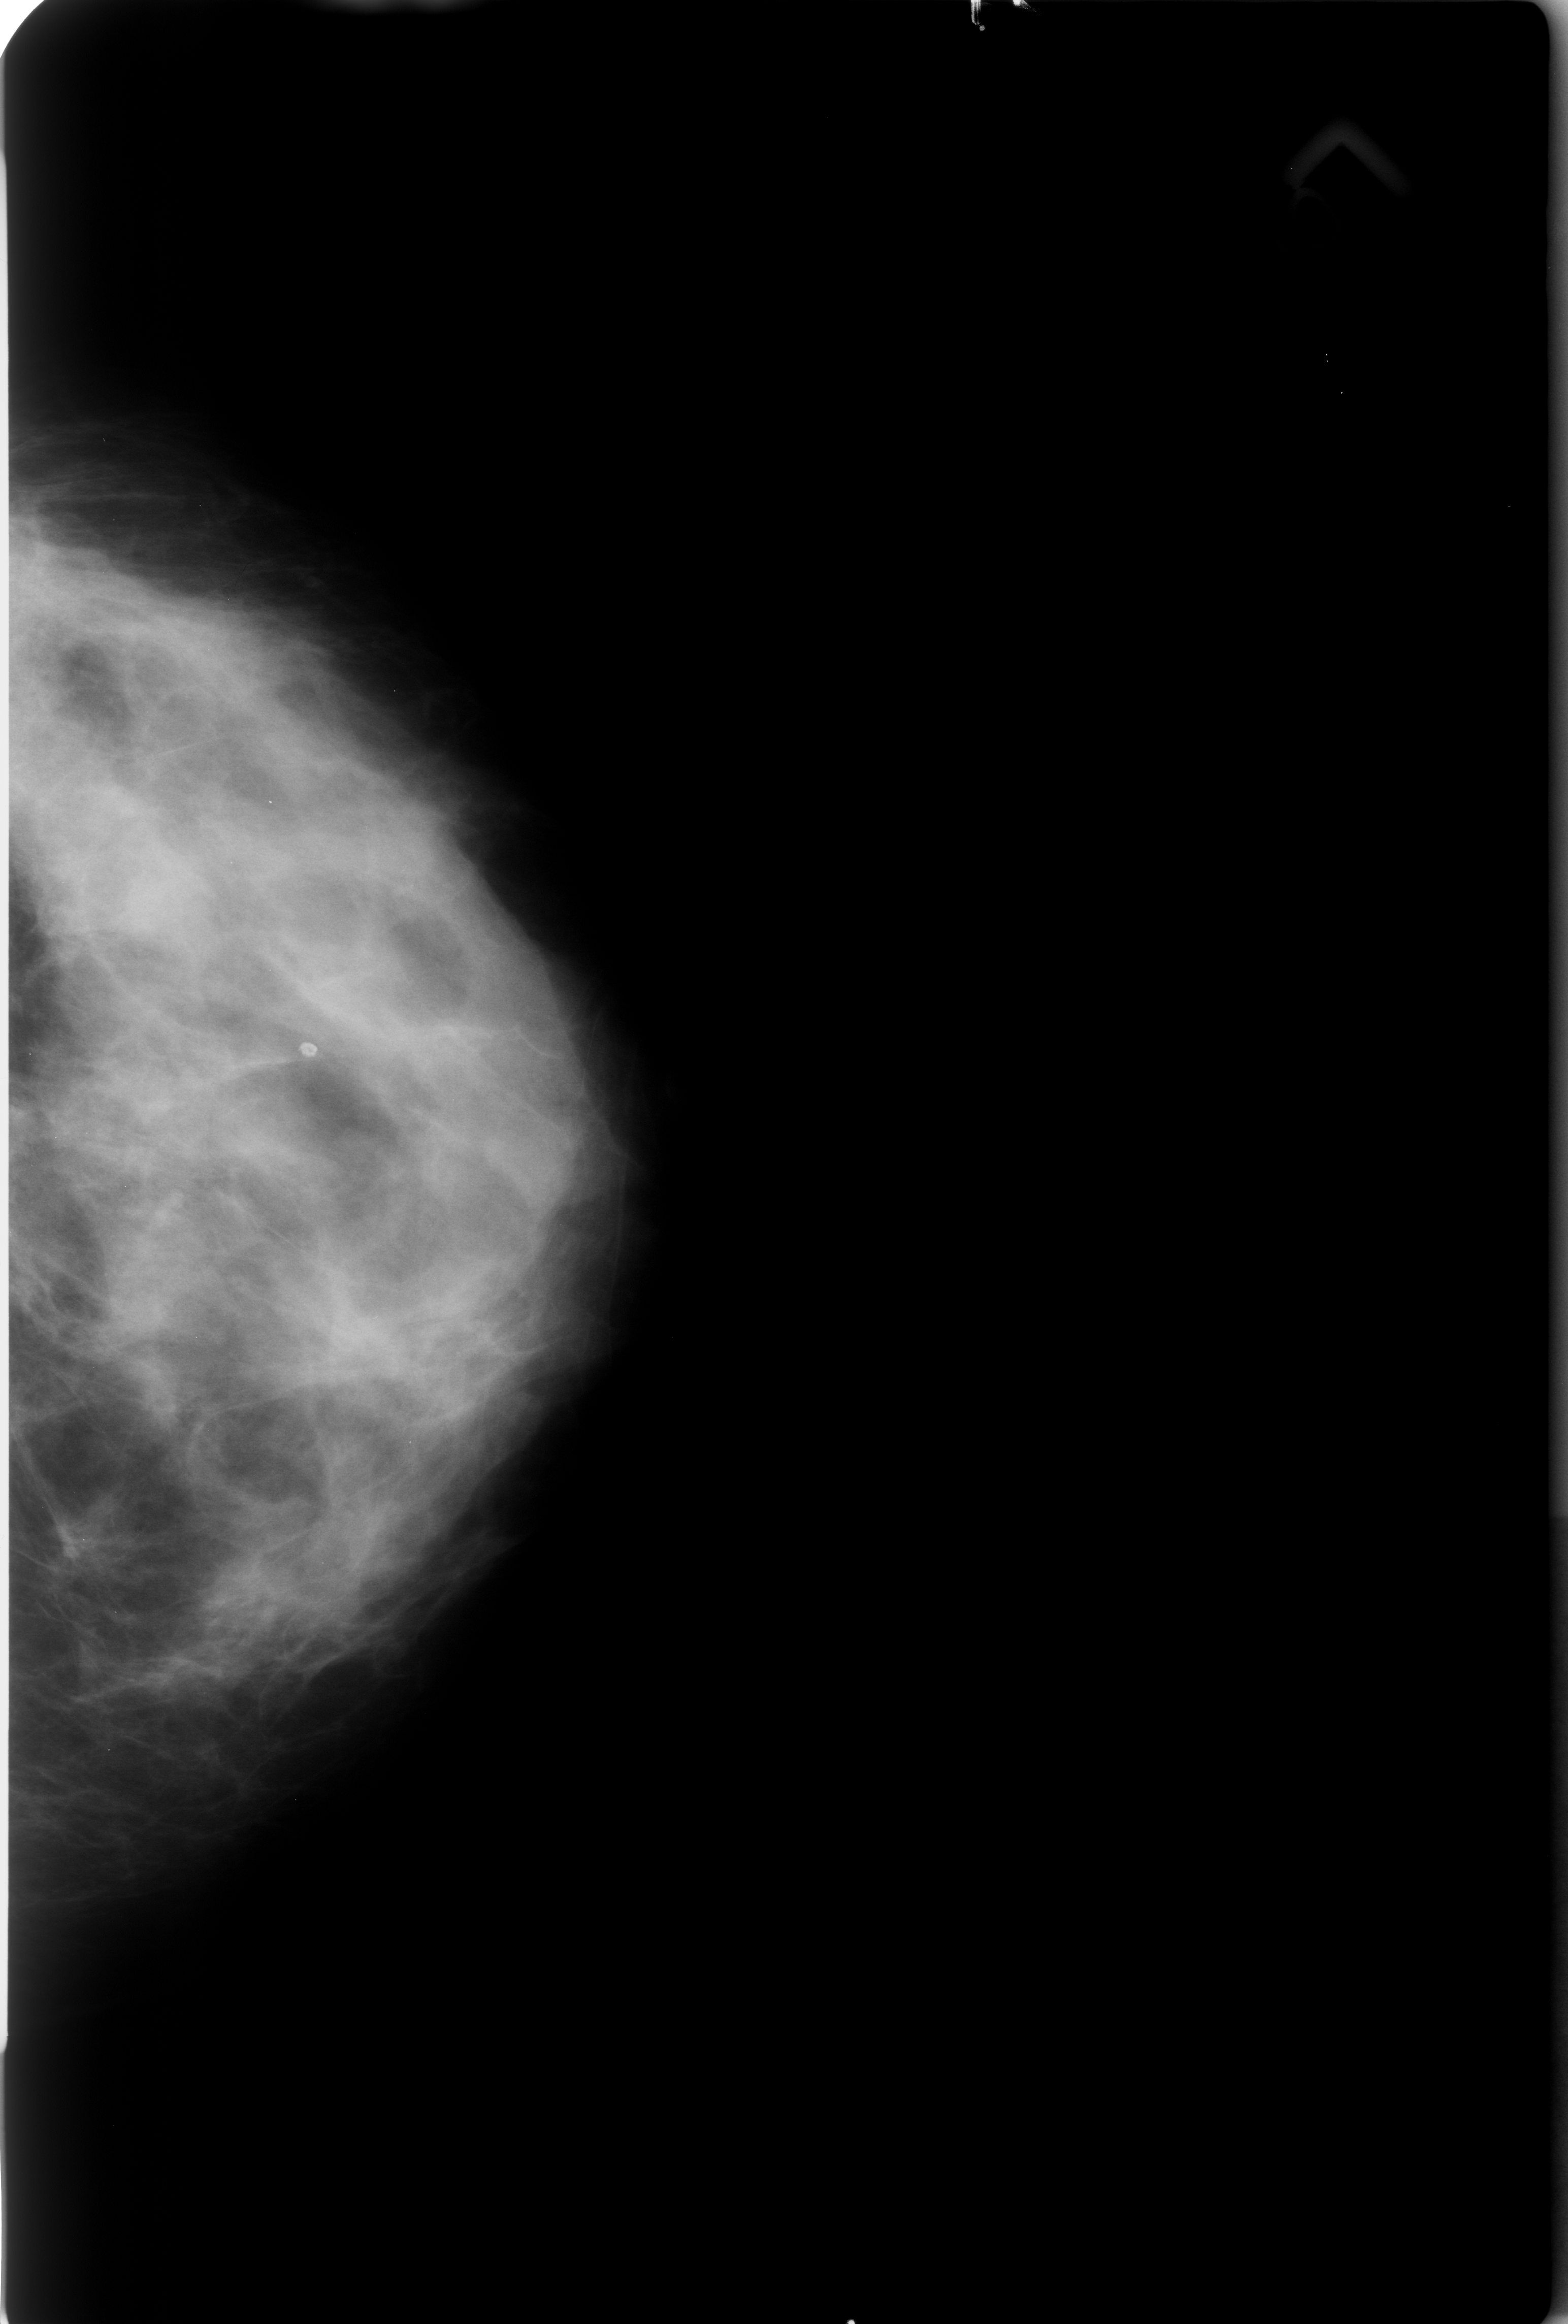
Scanned film-screen mammogram, left breast, CC view.
- Calcifications, morphology lucent center; BI-RADS assessment category 2; subtlety rating 4 on a 1 (subtle) to 5 (obvious) scale; benign; no additional work-up was recommended (benign without callback).